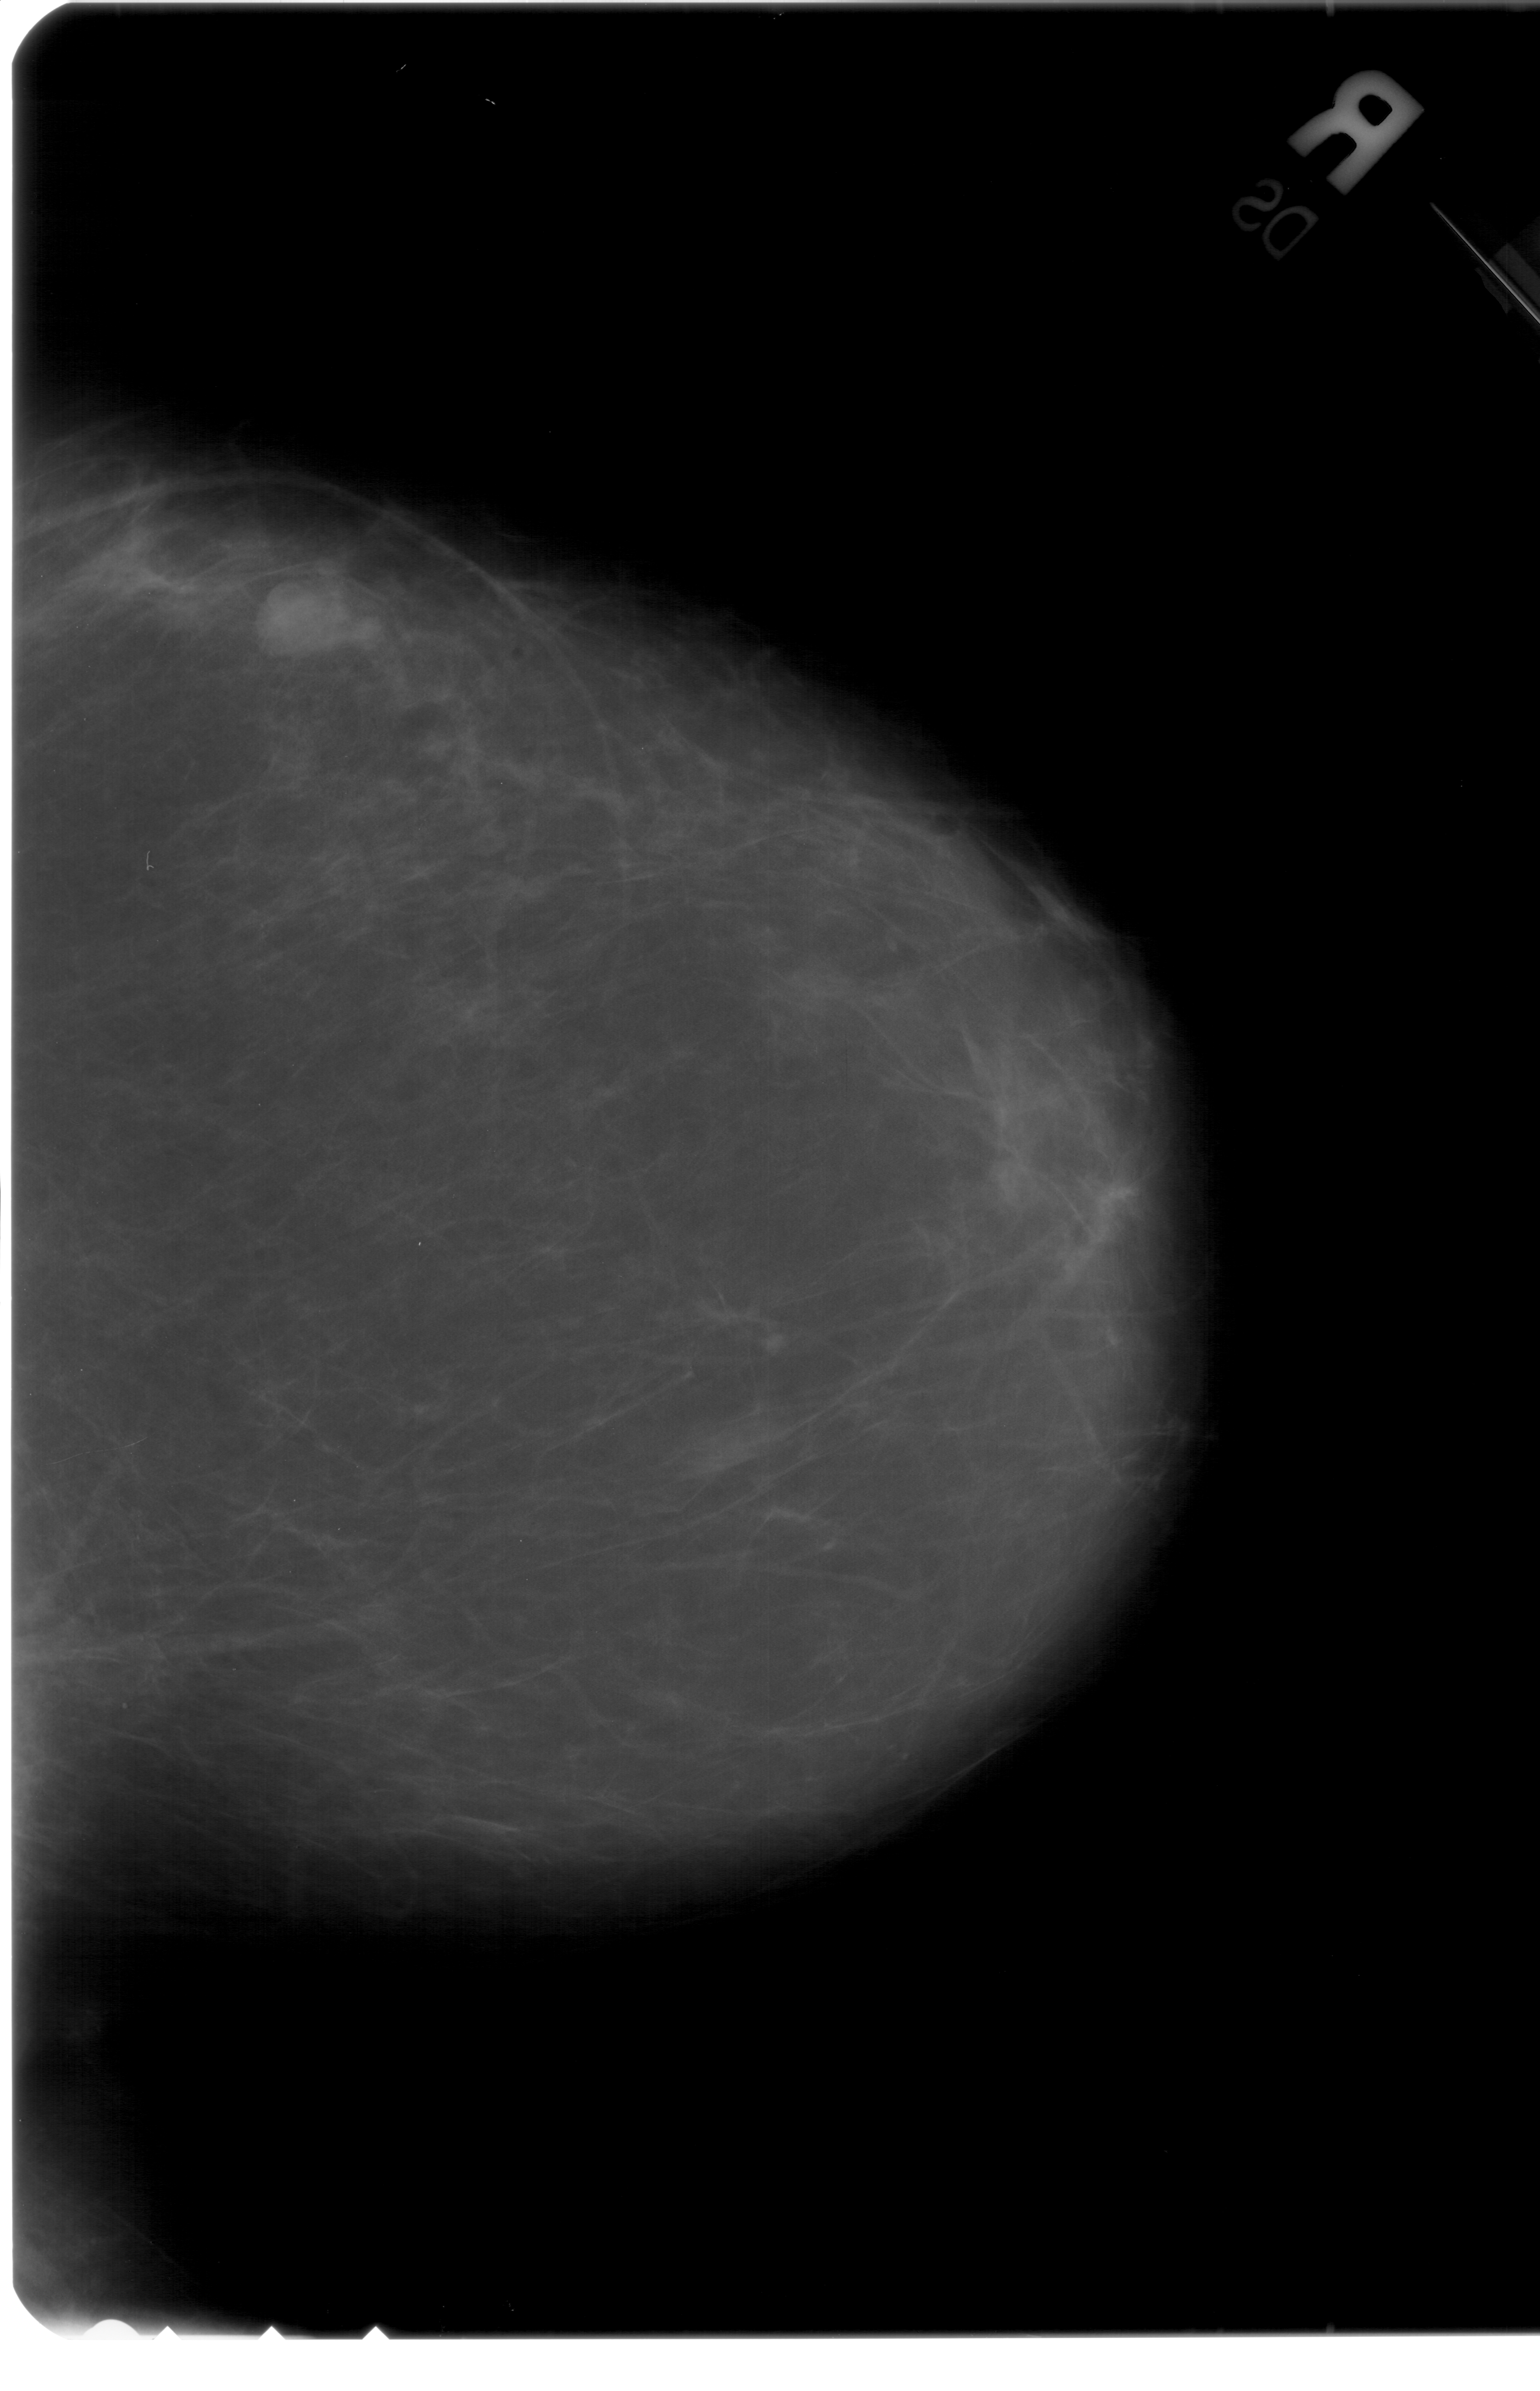
Digitized screen-film mammogram, right breast, craniocaudal (CC) view, BI-RADS breast density category 2 (scale 1–4).
Abnormality record for this image: mass, shape lobulated, margins circumscribed; BI-RADS assessment category 4; pathology result (as recorded, not read from the image): benign.